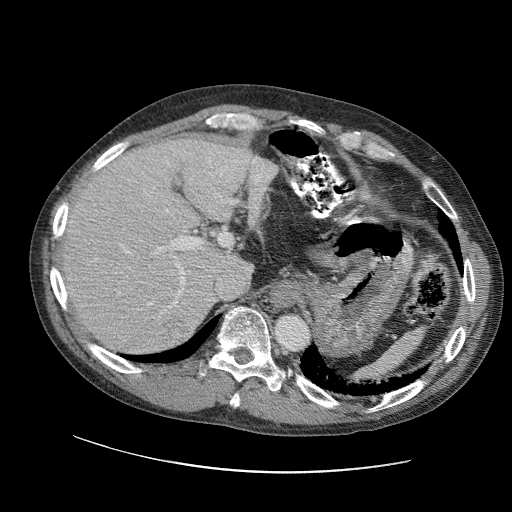
Contrast-enhanced abdominal CT (liver protocol), one axial slice; slice 75 of 109 in the series (ordered by position); reconstruction kernel STANDARD; 120 kVp; soft-tissue window (W 400 / L 40 HU); 2.5 mm slice thickness; 512 × 512 image matrix, field of view 400 × 400 mm. Case-level facts recorded for this patient, not image findings: diagnosis: hepatocellular carcinoma (patient treated with transarterial chemoembolisation; whether this scan precedes or follows treatment is not stated here); TNM stage (as recorded): Stage-IIIC; Child-Pugh class: B; tumour differentiation: well differentiated.
Structures marked on this image (semi-automatically segmented with operator editing):
- abdominal aorta: bounding box [x1, y1, x2, y2] px = [275, 314, 309, 350]
- liver parenchyma outside the tumour (the mass and vessels are separate outlines, so this box may not span the whole liver): [56, 136, 259, 352]
- mass: [164, 321, 195, 344]
- liver vessels: [94, 149, 250, 333]